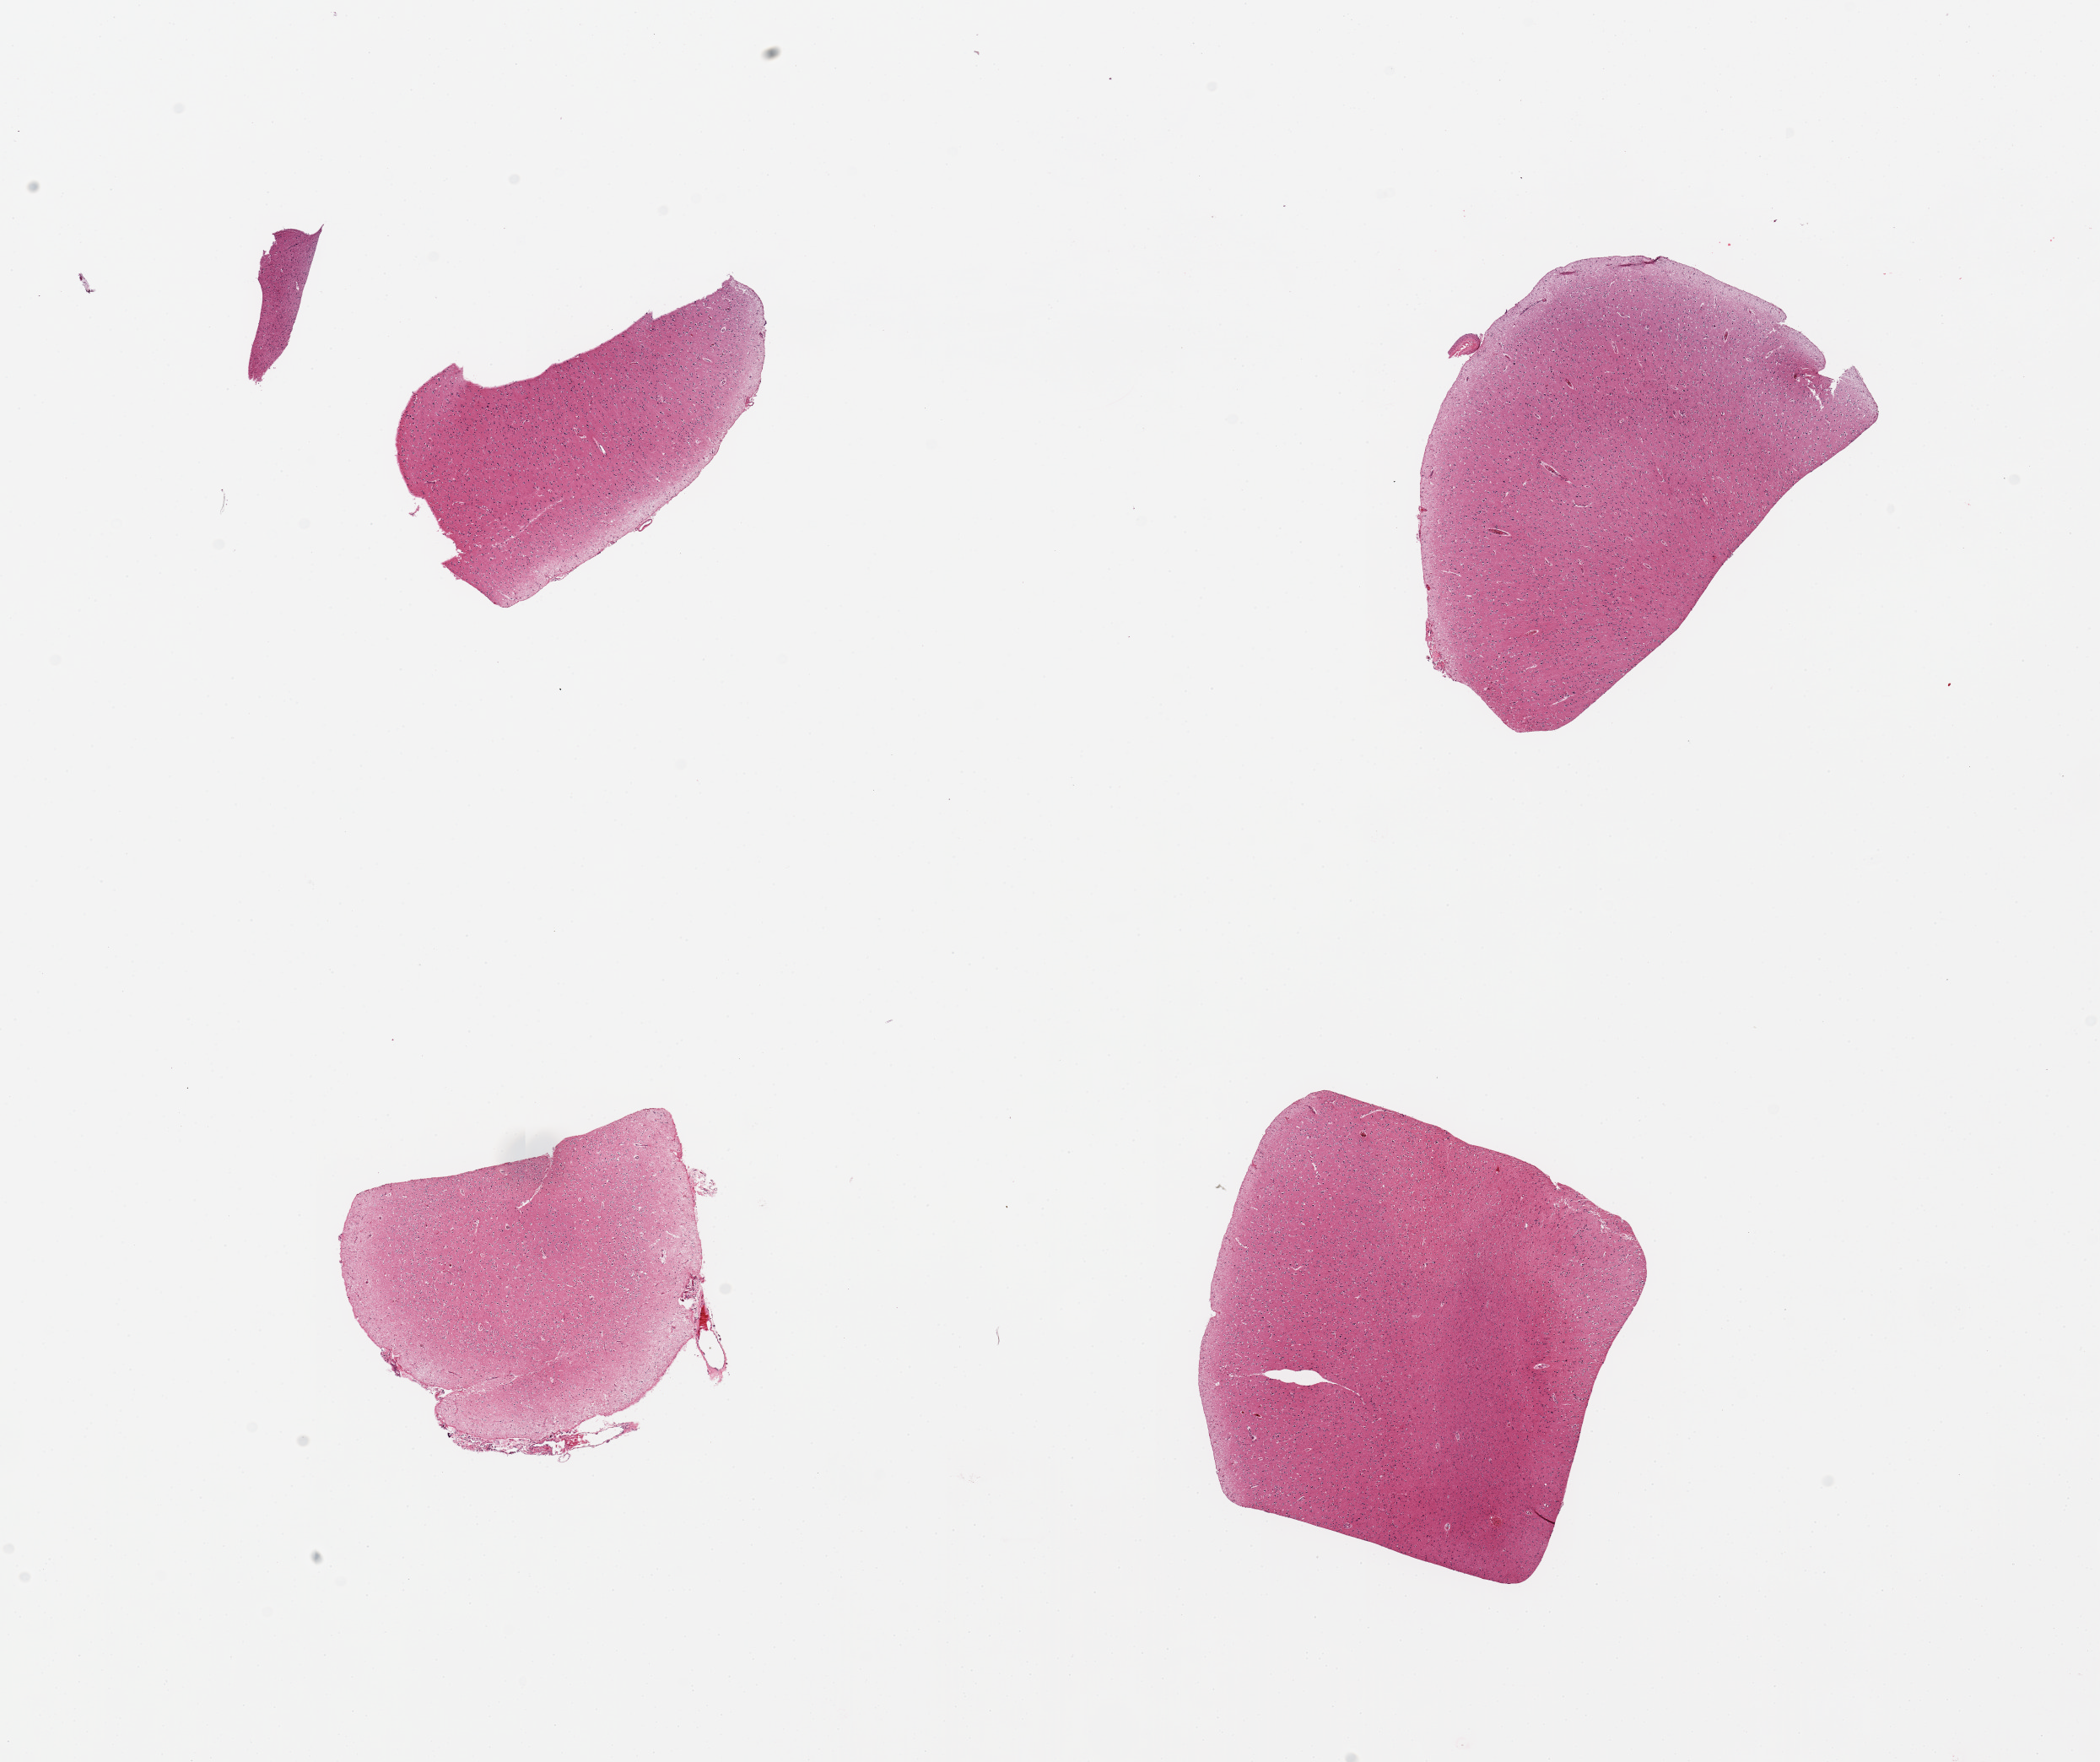
Digitized H&E-stained section, shown as a low-resolution overview of the whole scanned area (about 19.7 x 16.5 mm); PAXgene-fixed, paraffin-embedded tissue; section of cerebral cortex (target tissue); tissue donor sample. Donor: male.
Review note (as recorded): 4 pieces; mild to focally moderate autolysis.